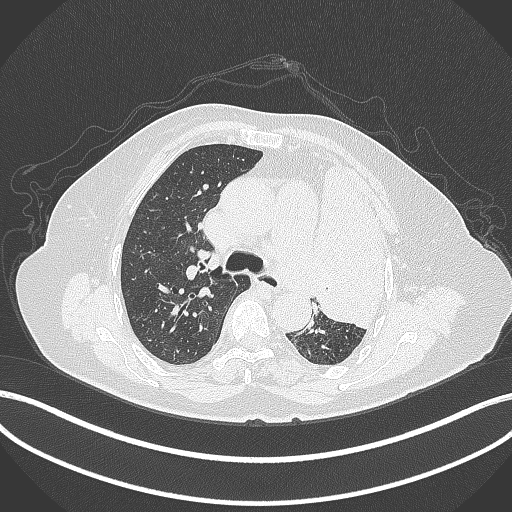
Chest CT, one axial slice. Position 257 of 399 along the scan axis. 120 kVp. Lung window (W 1500 / L -600 HU). 512 × 512 image matrix, field of view 400 × 400 mm. Female patient, age 75 years. Case-level facts recorded for this patient, not image findings: clinical TNM (as recorded): T3 N3 M1.
Annotated regions visible in this slice (rectangle marked by the reading radiologist):
- lung tumour (recorded histology: adenocarcinoma): bounding box <314,151,383,338> (left, top, right, bottom; pixels)